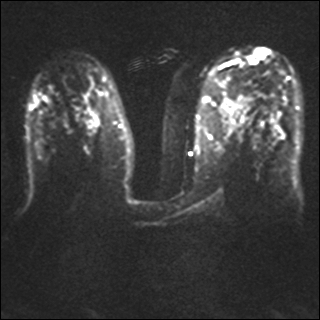
Breast MRI, one axial slice; diffusion-weighted series; image 2 of 4 stored at this slice position (different b-values; order by instance number); 1.5 T; 4 mm slice thickness; 320 × 320 image matrix, field of view 330 × 330 mm. Female patient.
Annotated regions visible in this slice (outlined manually by an expert reader):
- tumour on diffusion-weighted imaging: bounding box [x1, y1, x2, y2] px = [248, 51, 265, 63]